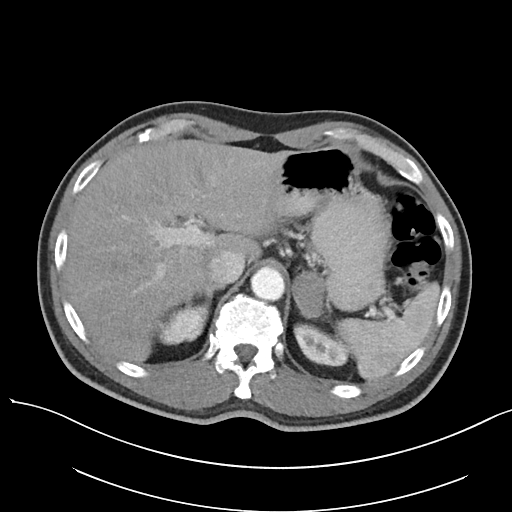
Contrast-enhanced abdominal CT, one axial slice; position 81 of 138 along the scan axis; reconstruction kernel I30f/3; 120 kVp; intravenous contrast given; soft-tissue window (W 400 / L 40 HU); 512 × 512 image matrix, field of view 400 × 400 mm. Patient: male, 63 years. From the clinical record (not read from this slice): diagnosis: adrenocortical carcinoma; tumour side: left adrenal; tumour size at pathology: 4.5 cm; Ki-67 index: 12 %; stage (as recorded): 1.
Annotated regions visible in this slice (semi-automatically segmented with operator editing):
- mass: bounding box [x1, y1, x2, y2] px = [292, 274, 324, 317]